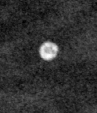
Cropped region of a digitized screen-film mammogram centred on a radiologist-marked abnormality; left breast; MLO view.
- Calcifications, morphology lucent centered; BI-RADS assessment category 2; subtlety rating 3 on a 1 (subtle) to 5 (obvious) scale; benign; no additional work-up was recommended (benign without callback).